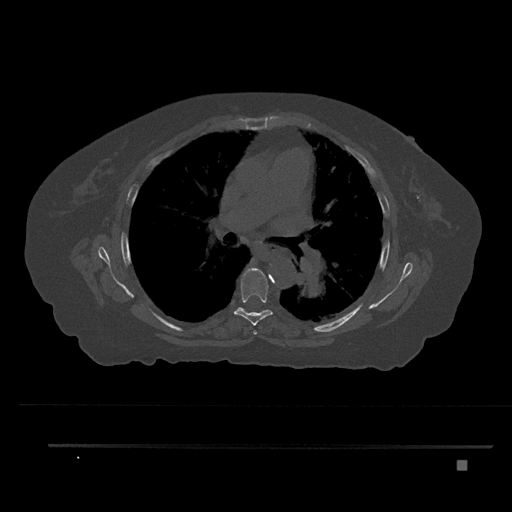
CT including the spine, one axial slice. Position 528 of 797 along the scan axis. Reconstruction kernel Br40s/3. 120 kVp. Bone window (W 1800 / L 400 HU). 0.5 mm slice thickness. 512 × 512 image matrix. Female patient, age 76 years. From the clinical record (not read from this slice): primary cancer: lung; vertebrae with lytic lesions (as recorded): T11, L3.
Outlined on this slice (semi-automatically segmented with operator editing):
- T5 vertebra: bounding box <247,268,257,335> (left, top, right, bottom; pixels)
- T6 vertebra: <234,268,273,326>